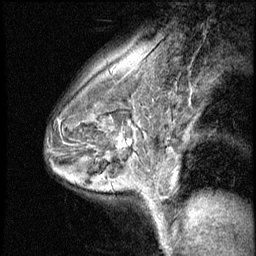
Breast MRI (dynamic contrast-enhanced), one sagittal slice. Slice 41 of 56 in the series (ordered by position). 3 images stored at this slice position (order not interpretable as contrast timing). 1.5 T. TE 4.2 ms, TR 8.7 ms. 2.5 mm slice thickness. 256 × 256 image matrix. Patient: female, 43 years. Case-level facts recorded for this patient, not image findings: setting: breast cancer imaged before/during neoadjuvant chemotherapy; receptor status: HR-positive, HER2-negative.
Structures marked on this image (semi-automatically segmented with operator editing):
- analysis volume of interest (the breast-tissue region the enhancement analysis was run in; not a lesion): bounding box (x1, y1, x2, y2) in pixels: (101, 120, 145, 165)
- tumour enhancement mask (voxels above the 140 % enhancement threshold inside the analysis volume of interest): (118, 138, 132, 144)